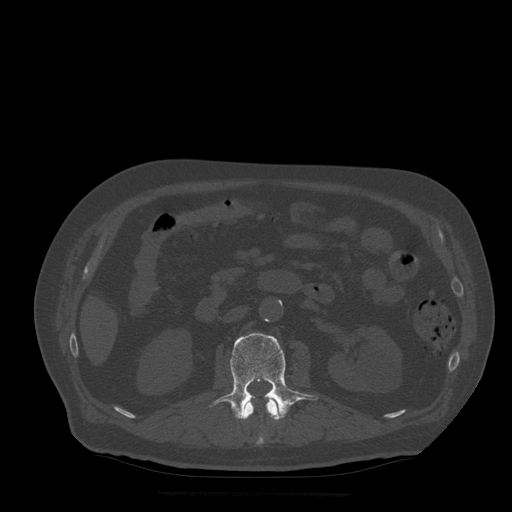
CT including the spine, one axial slice; slice 173 of 522 in the series (ordered by position); bone window (W 1800 / L 400 HU); 512 × 512 image matrix. Patient age 72 years. From the clinical record (not read from this slice): primary cancer: prostate.
Annotated regions visible in this slice (semi-automatically segmented with operator editing):
- L1 vertebra: bounding box <242,396,280,445> (left, top, right, bottom; pixels)
- L2 vertebra: <209,333,319,420>